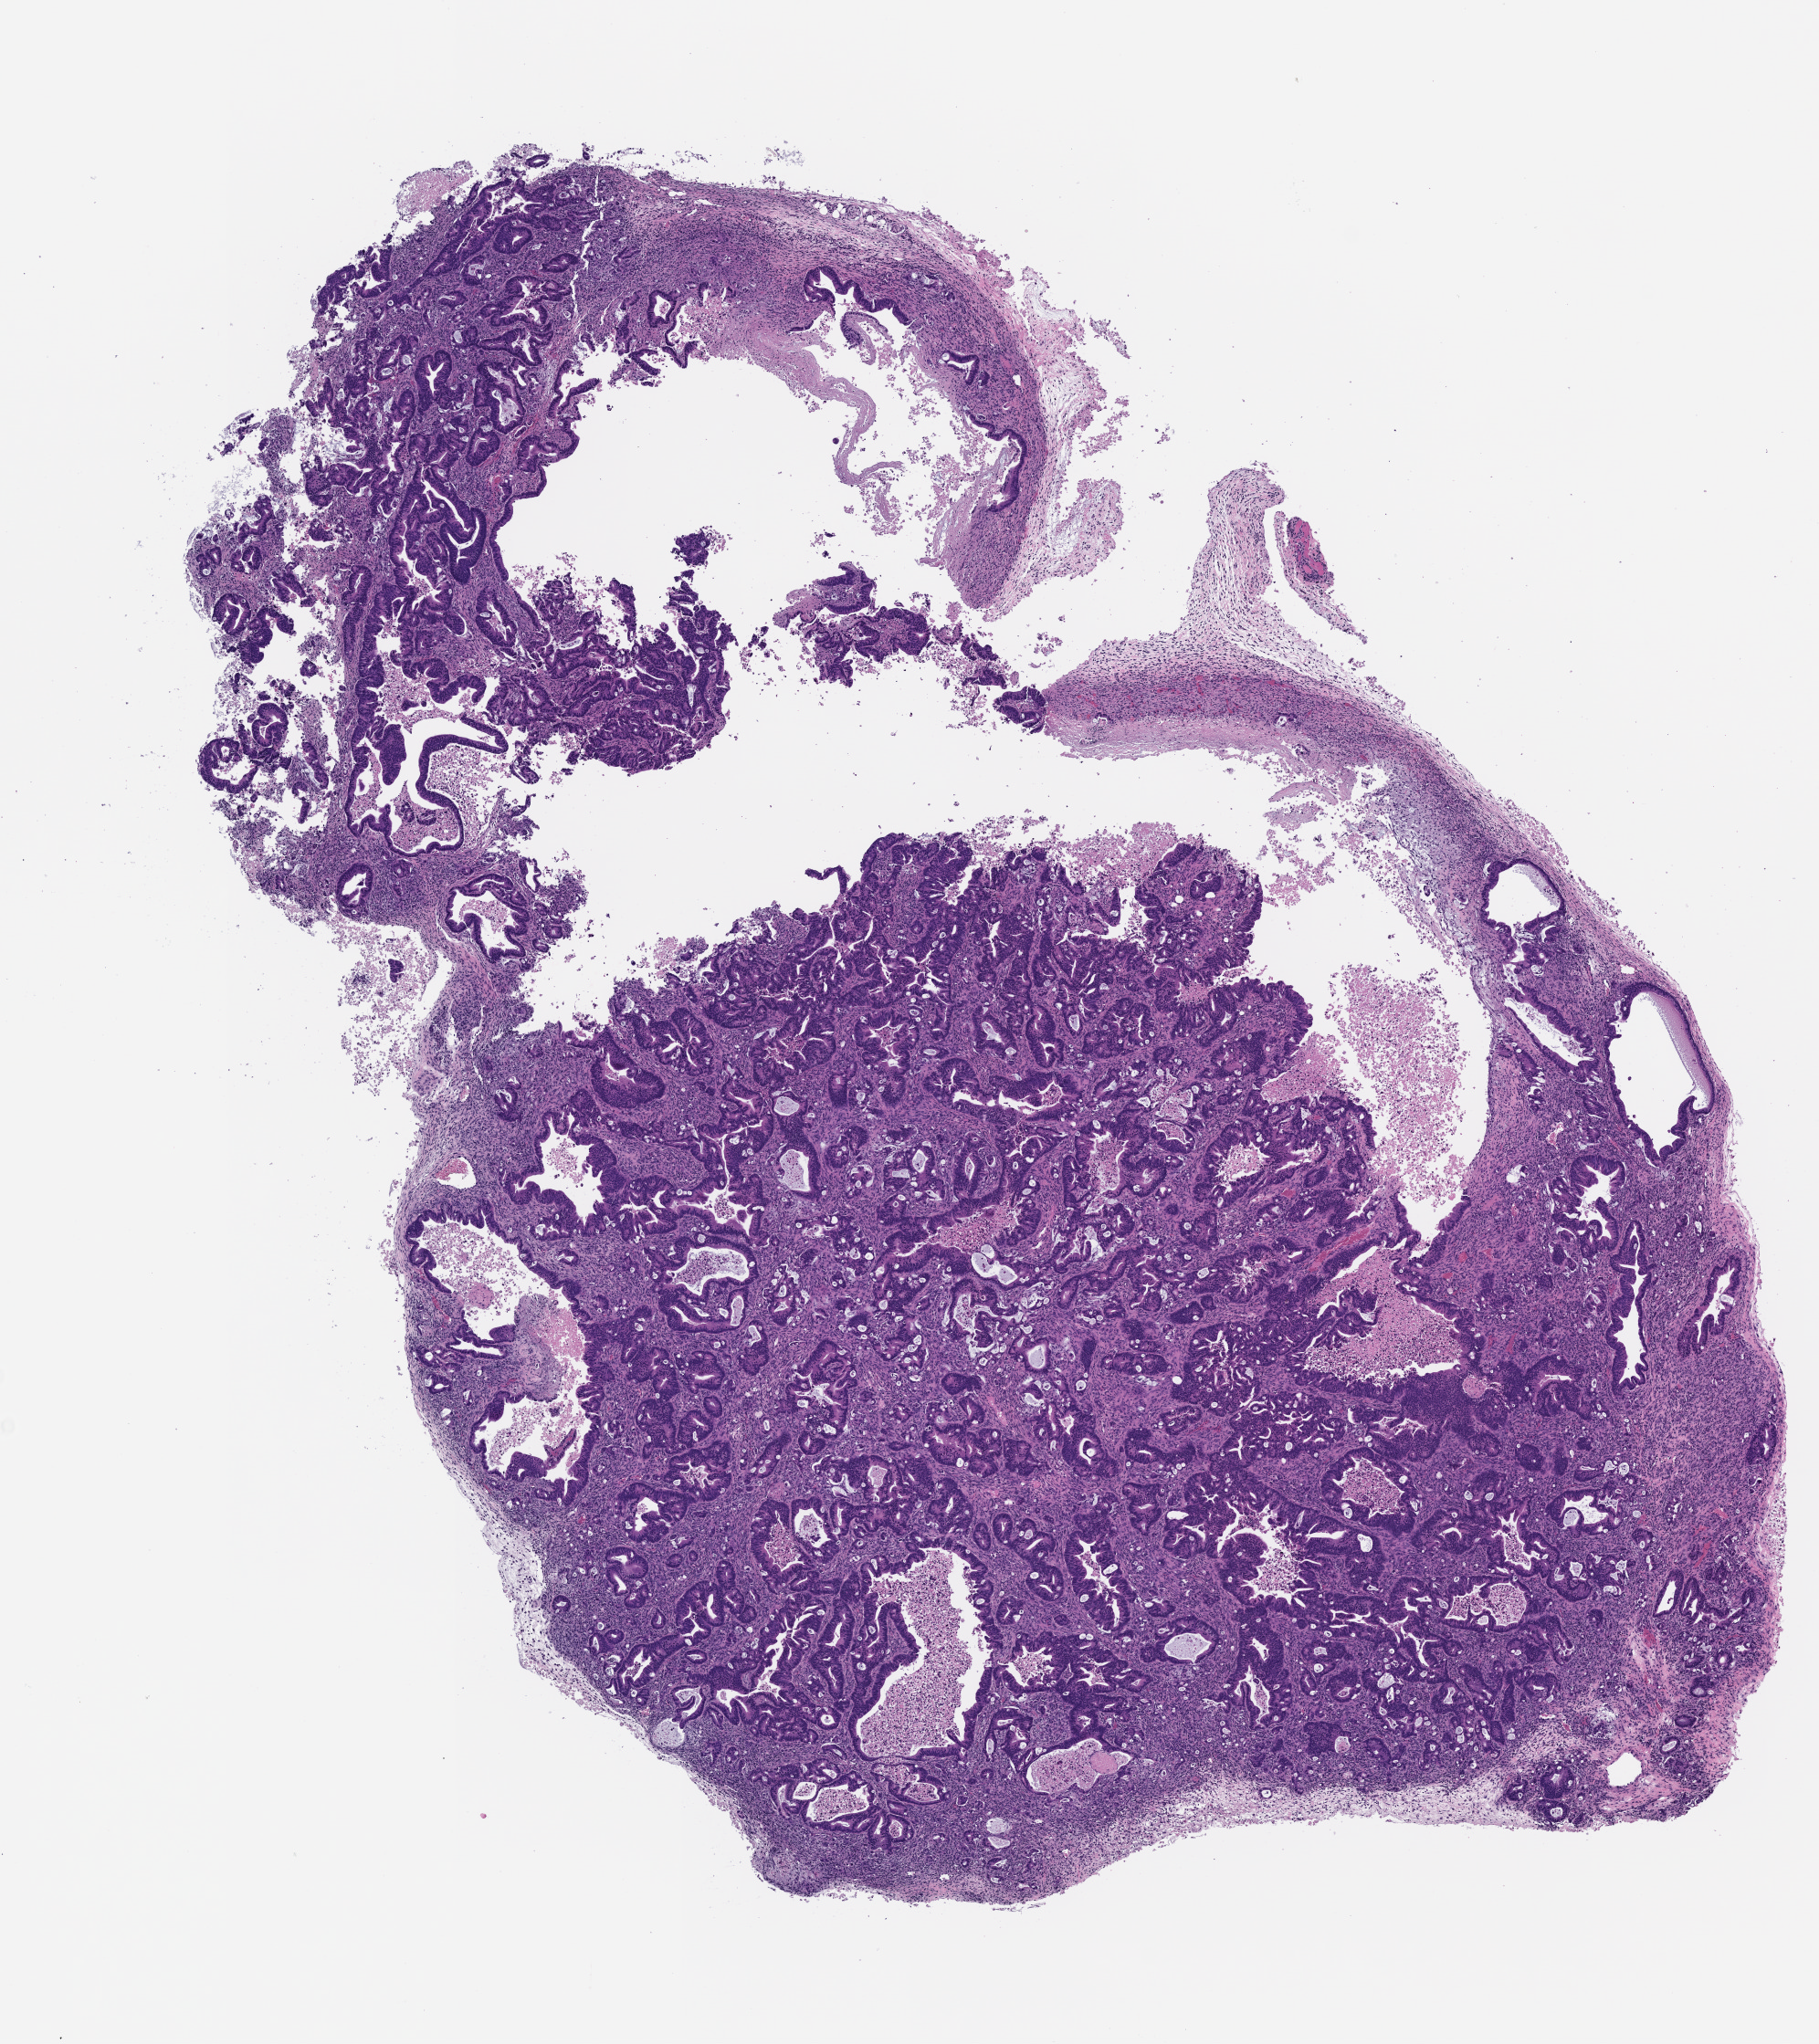
Whole-slide image, hematoxylin and eosin (H&E): patient-derived xenograft (human tumor grown in a mouse), passage 3 — a low-resolution overview of the entire scanned area, about 8.0 x 9.0 mm. Formalin-fixed, paraffin-embedded (FFPE) tissue. Originating tumor site category: rectum.
* originating patient diagnosis: Rectal Adenocarcinoma